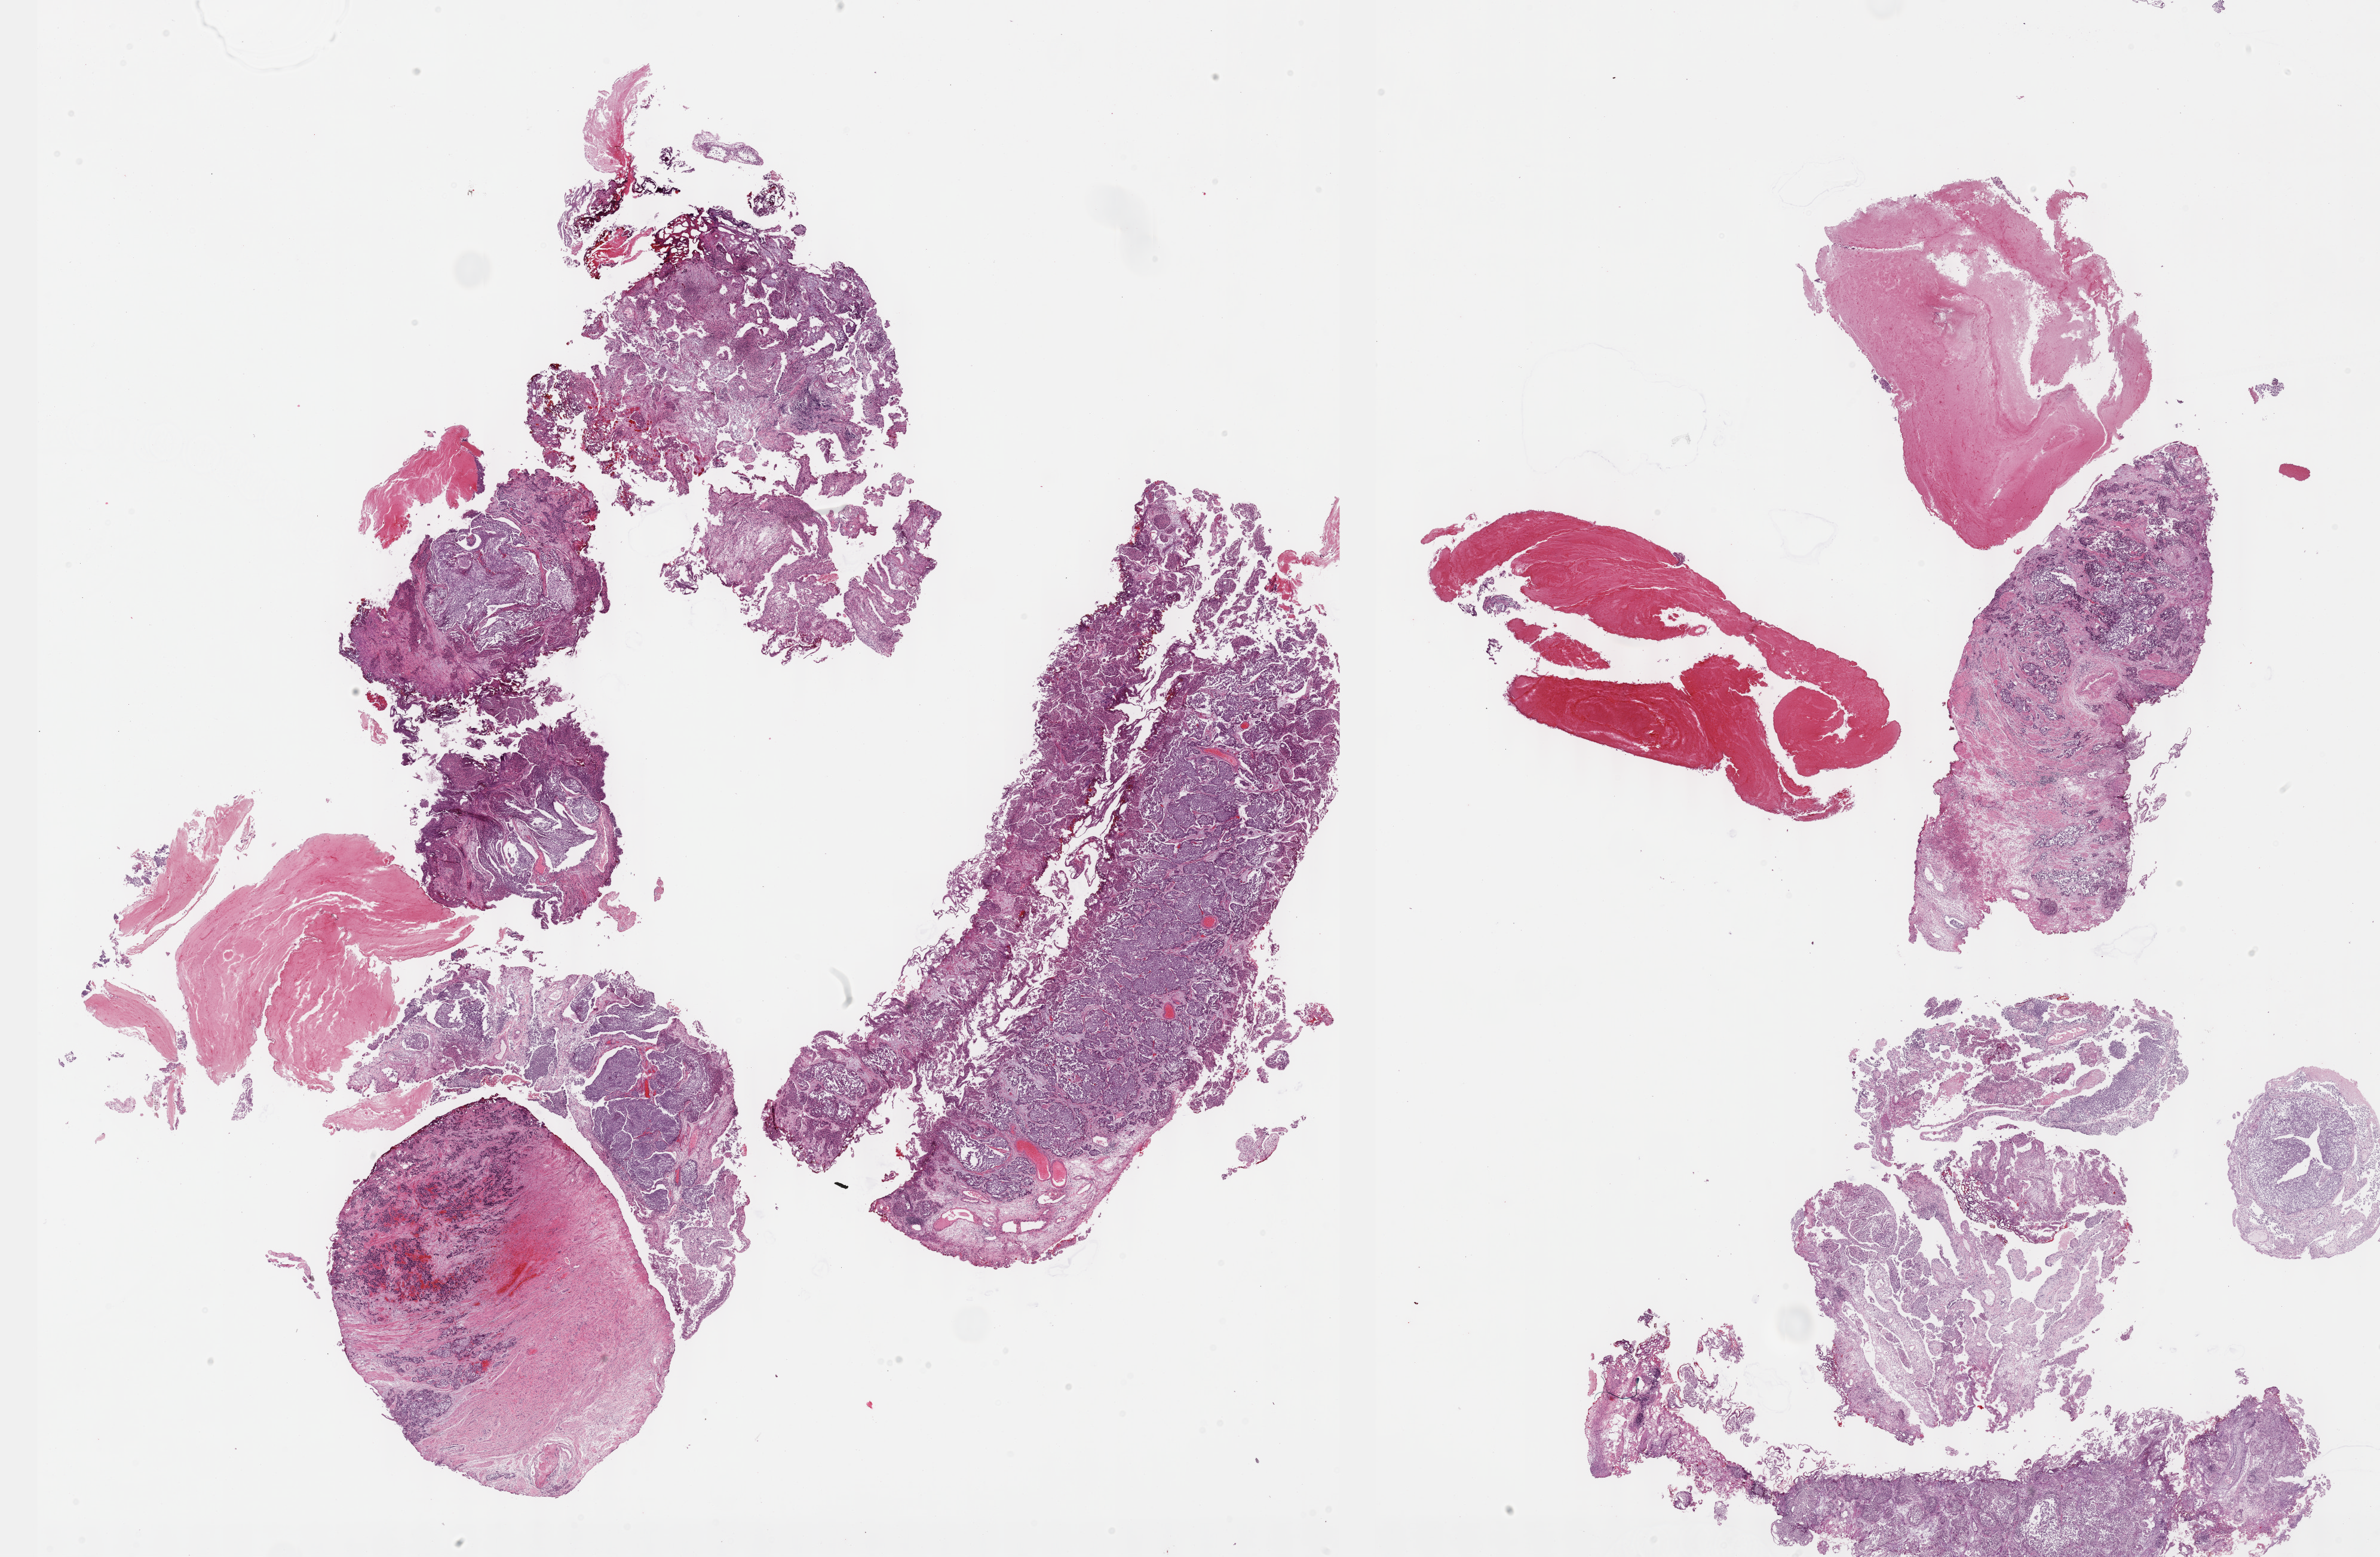
Whole-slide histology image, Hematoxylin and eosin (H&E) stained, whole scanned area (about 32.2 x 21.1 mm) shown as a low-resolution overview, formalin-fixed paraffin-embedded (FFPE) diagnostic section, sample: primary tumour, bladder. Male patient; age at initial diagnosis 68 years. Histologic grade: high grade.
• AJCC pathologic stage: IV (7th edition)
• TNM: T4a N2 MX
• diagnosis: Transitional cell carcinoma